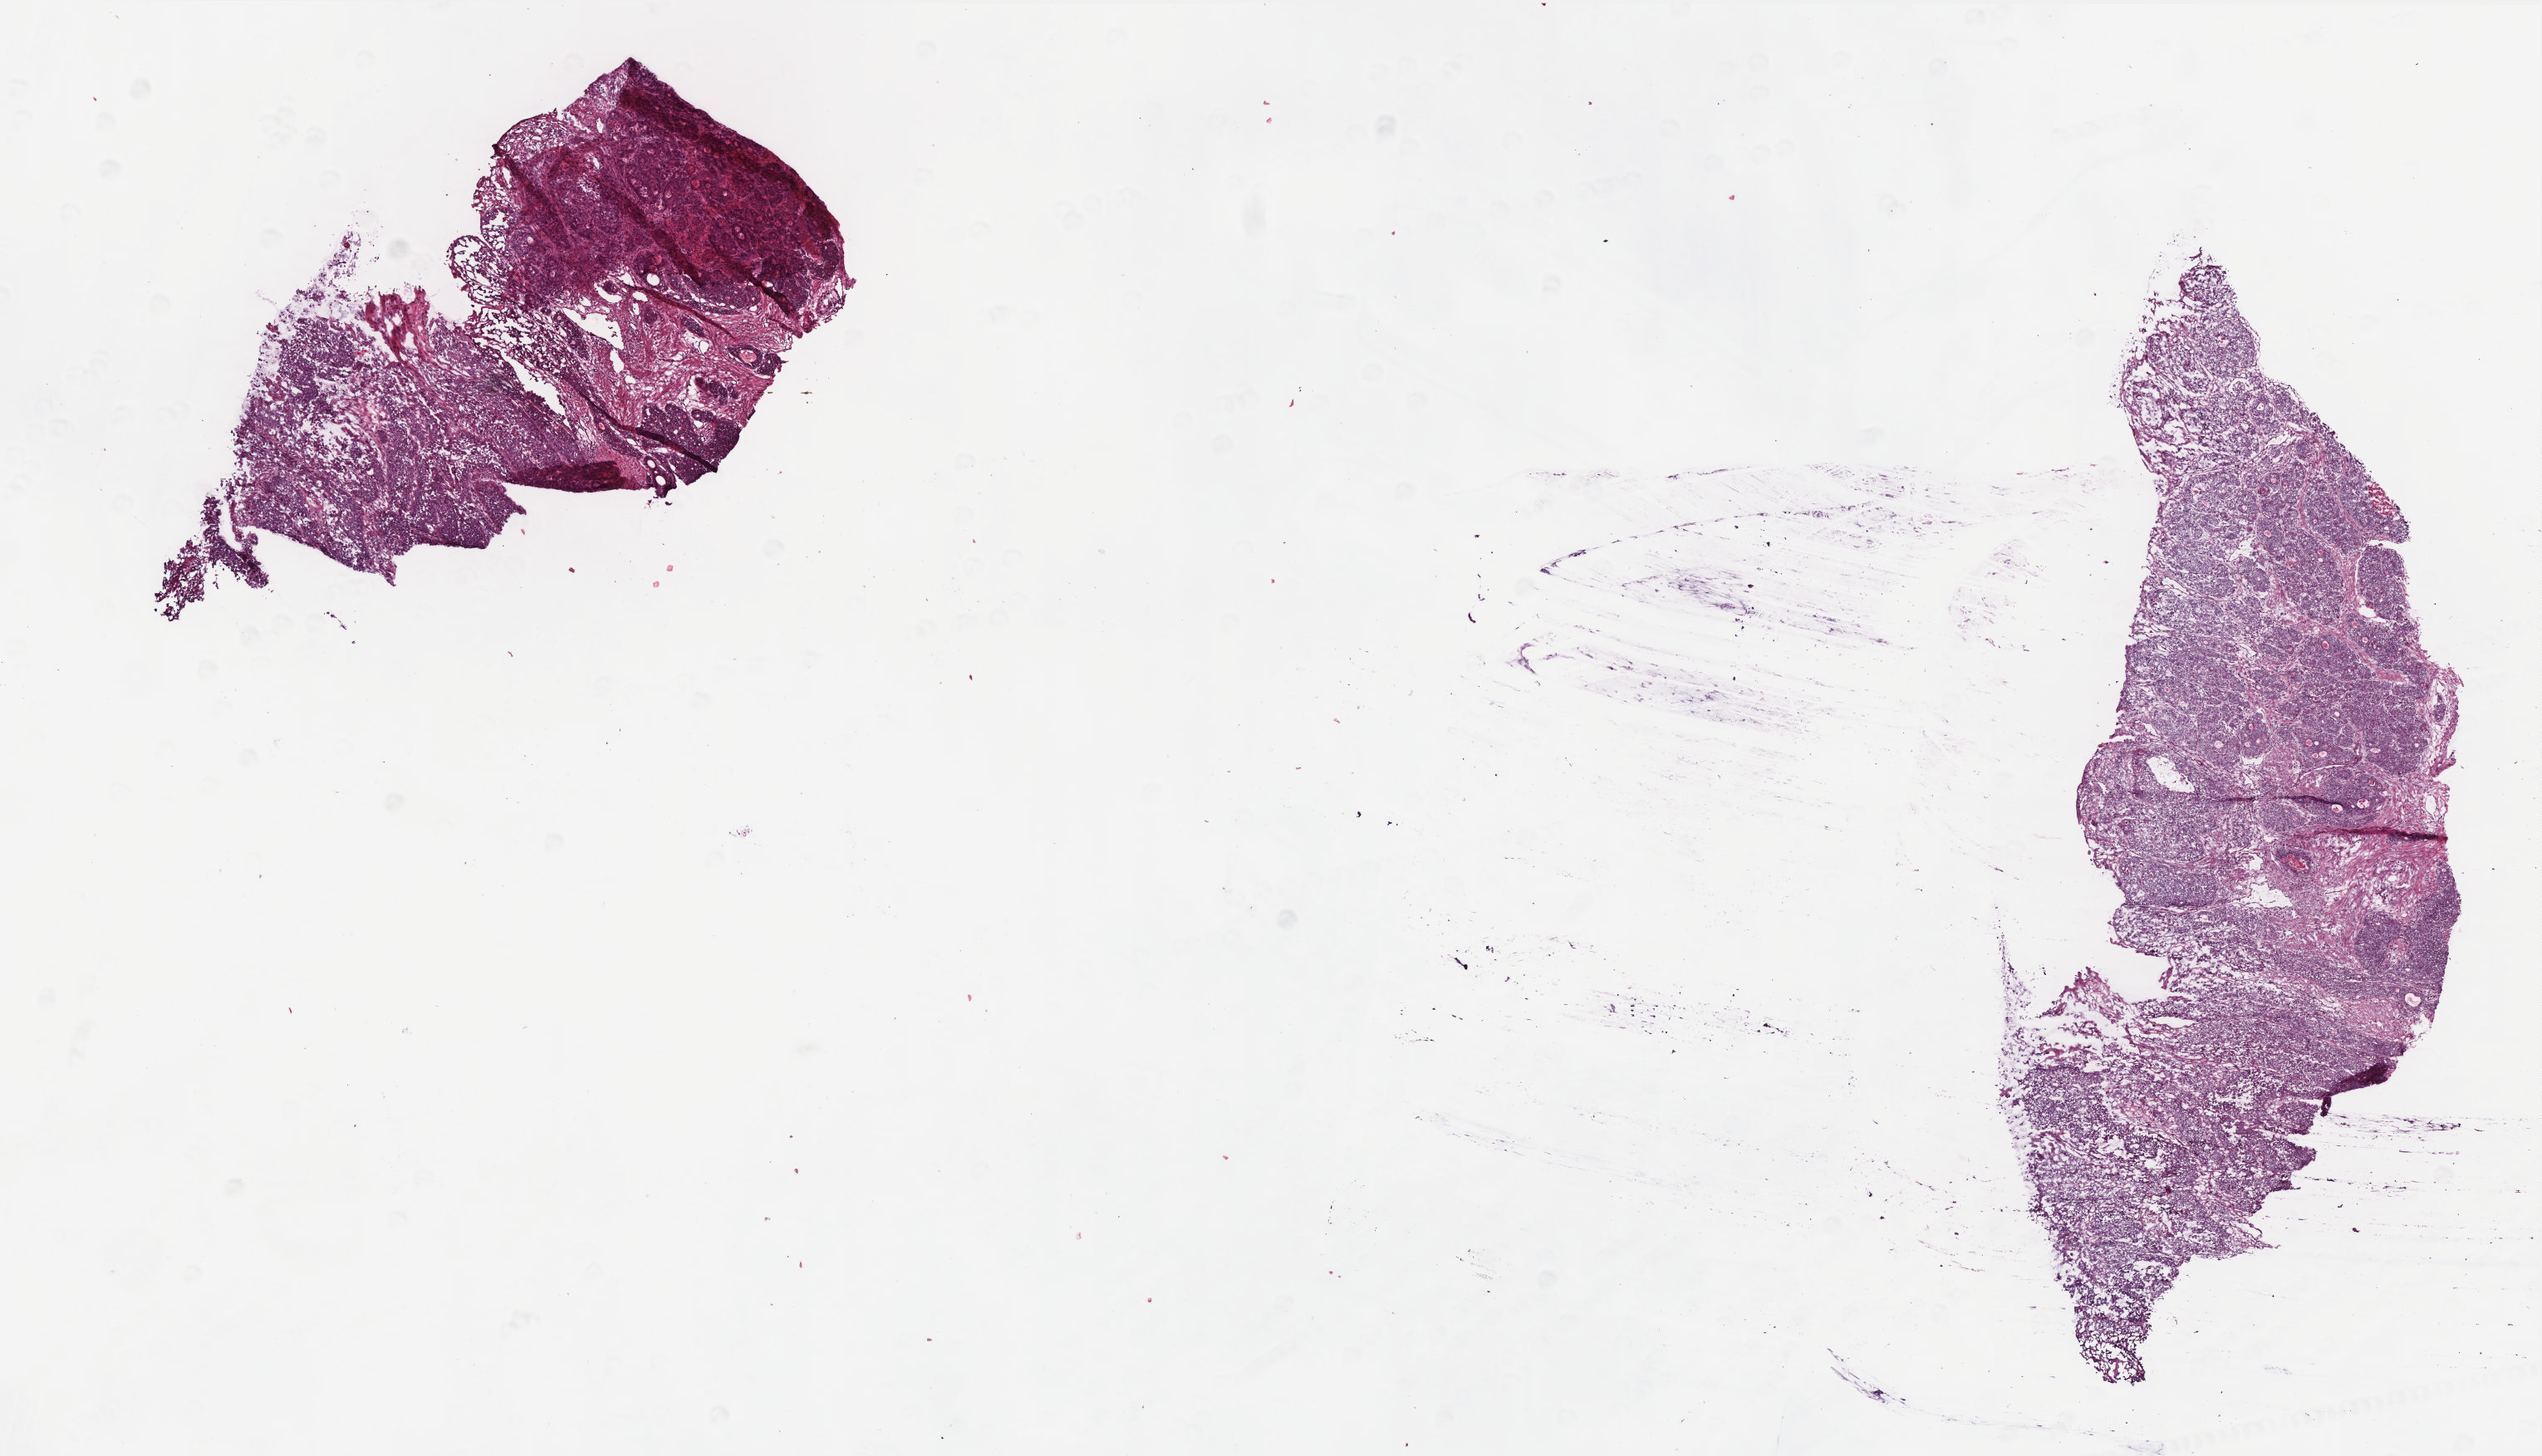
Whole-slide histology image, Hematoxylin and eosin (H&E) stained, shown as a low-resolution overview of the whole scanned area (about 12.3 x 7.0 mm); frozen section from the bottom of the tissue portion; primary tumour sample from the colon. Patient: female, age at initial diagnosis 83 years. Composition of this section per pathologist review: tumour cells 90%, tumour nuclei 95%.
Diagnosis: Adenocarcinoma, NOS (sigmoid colon).